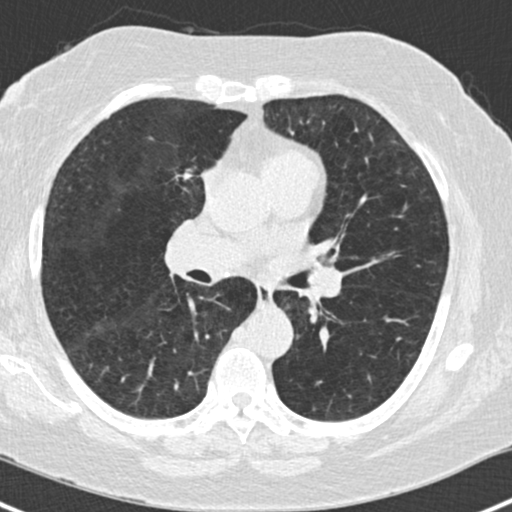
Low-dose screening chest CT, one axial slice. Position 84 of 168 along the scan axis. 120 kVp. Lung window (W 1500 / L -600 HU). 512 × 512 image matrix, field of view 303 × 303 mm.
Structures marked on this image (manually delineated by an expert):
- lesion 1 (tumor, upper lobe of right lung): bounding box (x1, y1, x2, y2) in pixels: (176, 168, 193, 181)